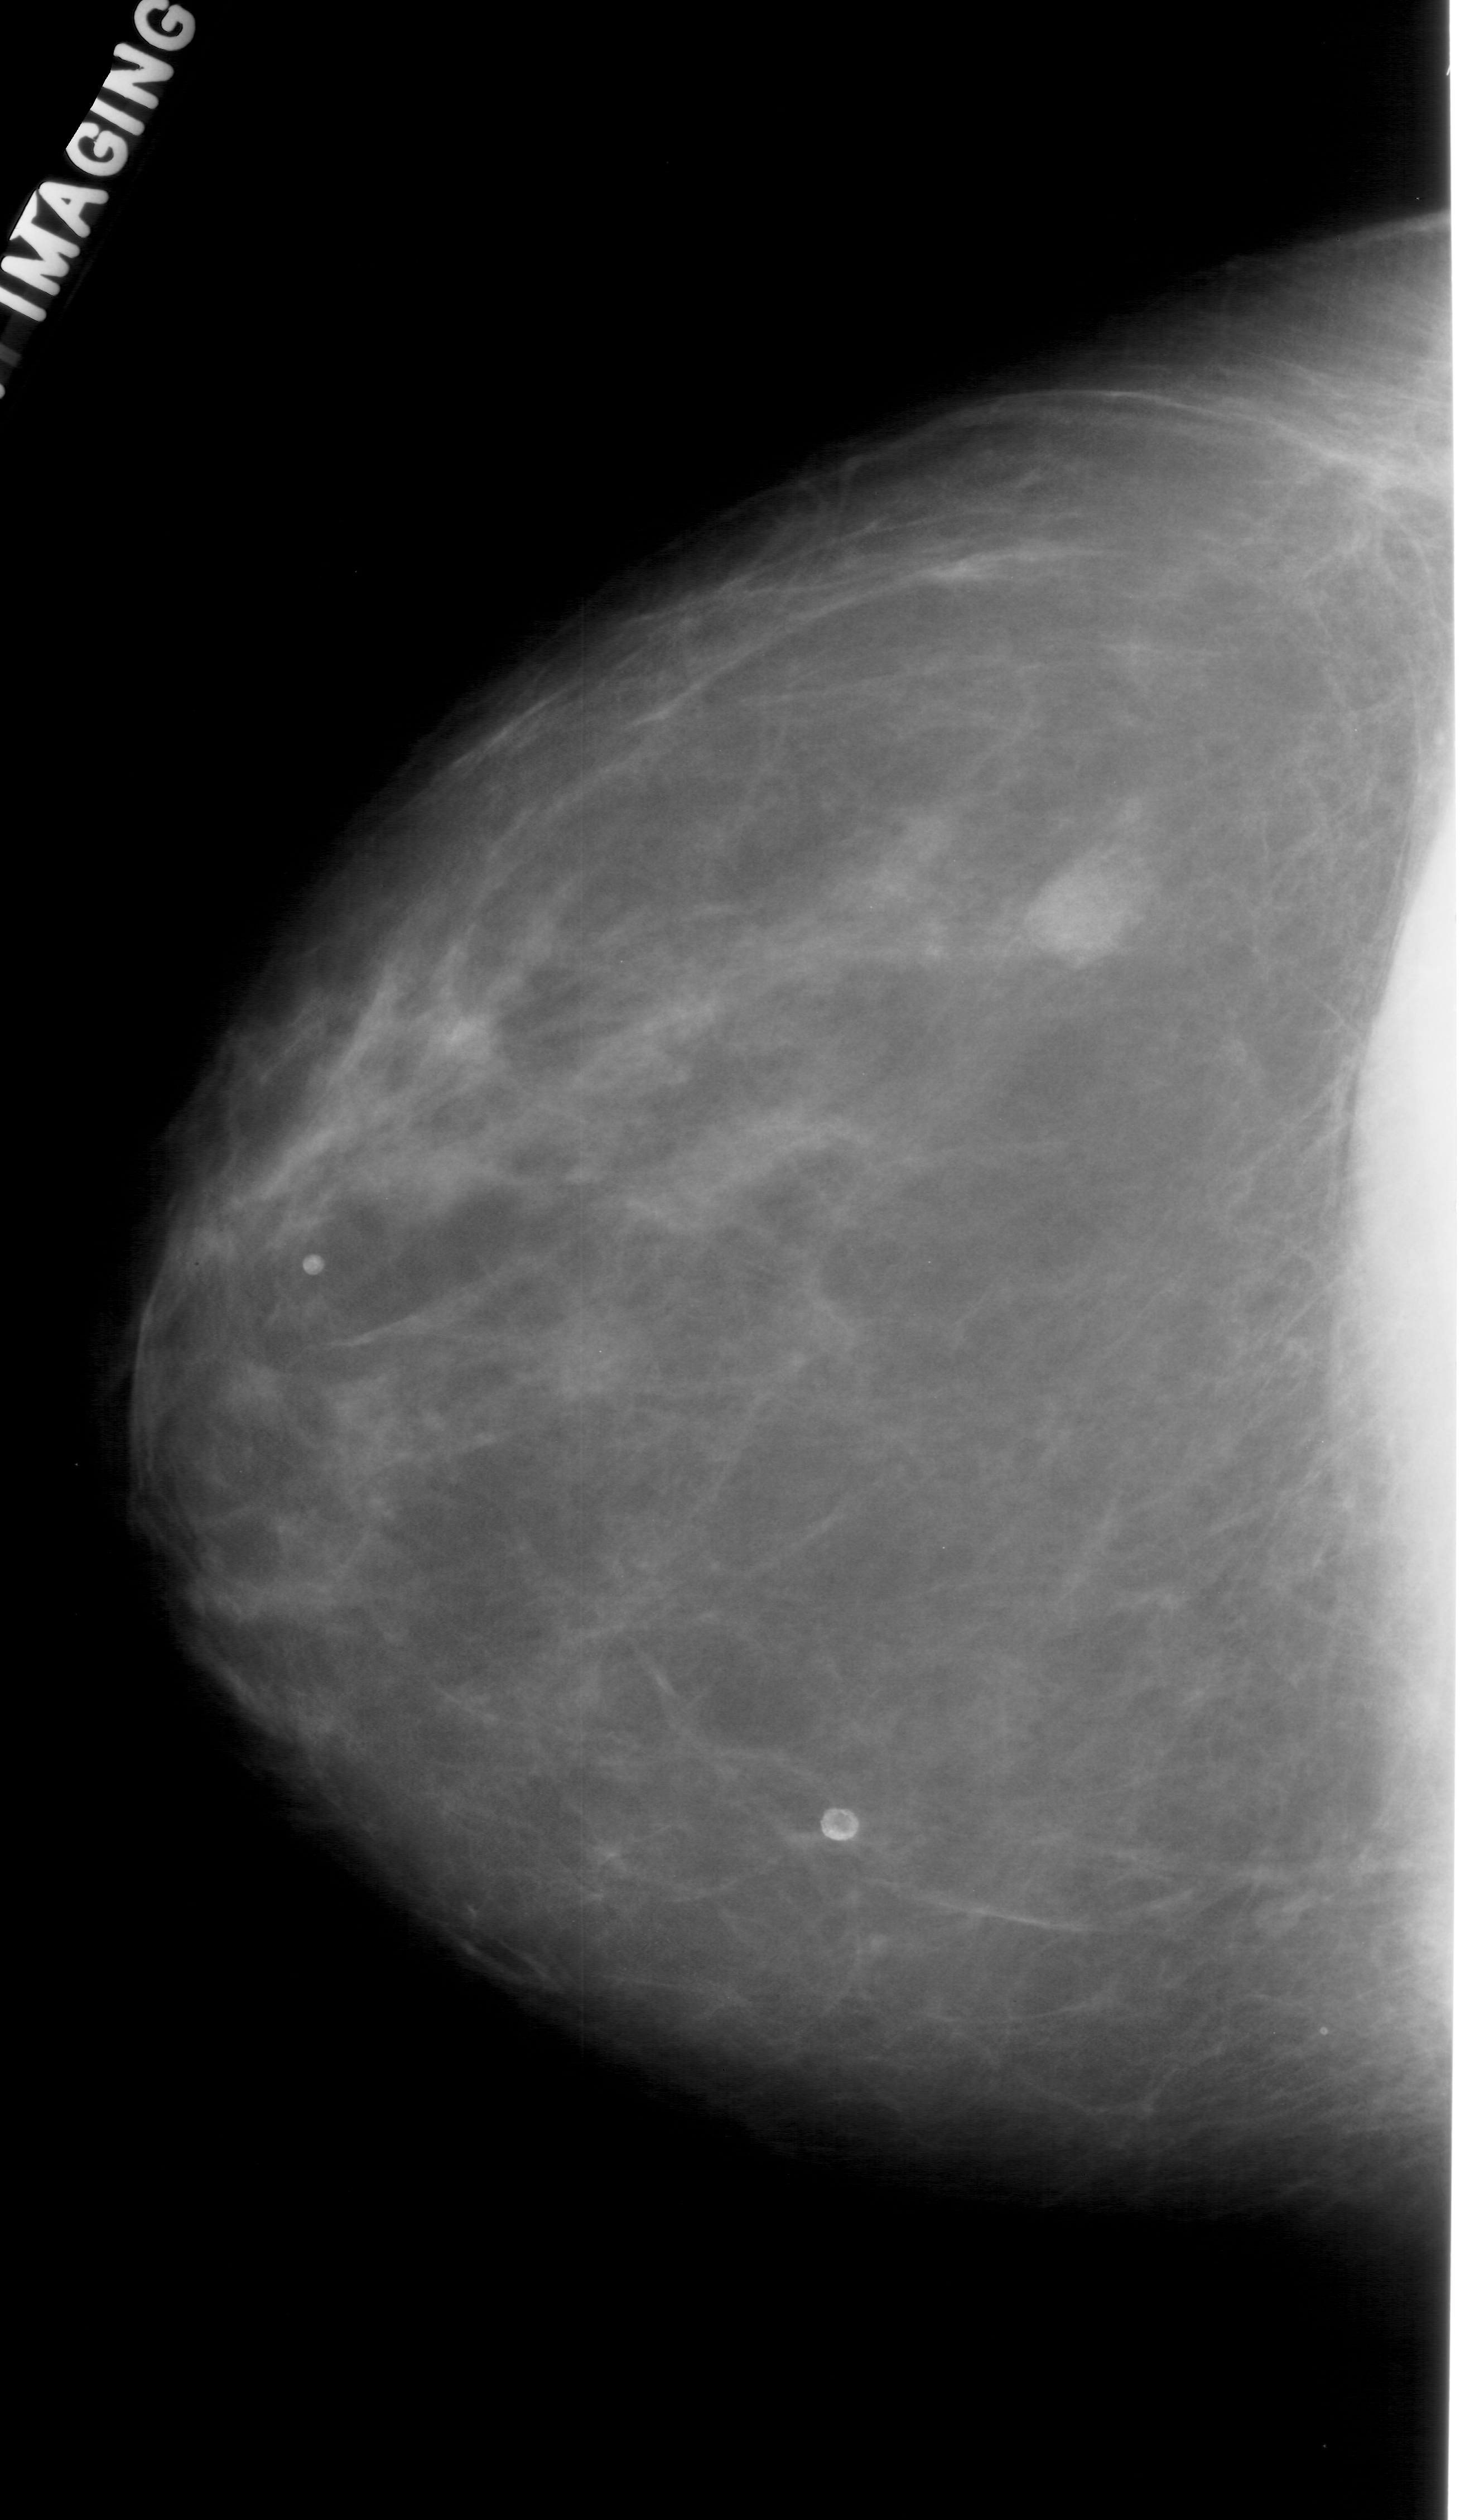
Digitized screen-film mammogram, left breast, craniocaudal (CC) view, breast composition: scattered fibroglandular densities (BI-RADS density category 2 of 4).
- Marked findings (only marked abnormalities are described; nothing is implied about the rest of the image): mass, shape lobulated, margins obscured; BI-RADS assessment category 4; subtlety rating 5 on a 1 (subtle) to 5 (obvious) scale; pathology (as recorded): benign.